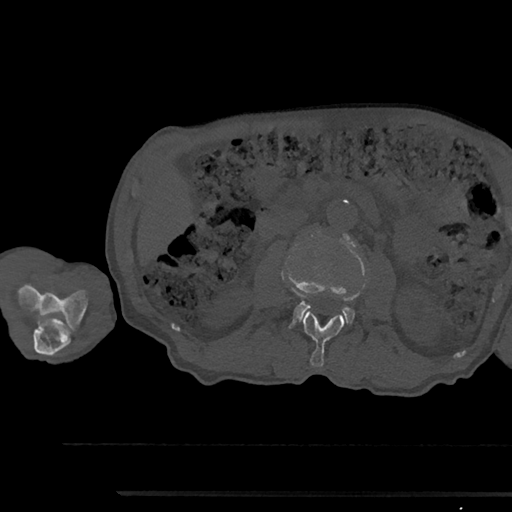
CT including the spine, one axial slice; slice 530 of 797 in the series (ordered by position); reconstruction kernel Br40s/3; bone window (W 1800 / L 400 HU); 0.5 mm slice thickness; 512 × 512 image matrix, field of view 367 × 367 mm. Male patient, age 79 years. Case-level facts recorded for this patient, not image findings: primary cancer: prostate.
Annotated regions visible in this slice (semi-automatic segmentation, software-assisted and operator-edited):
- L2 vertebra: bounding box [x1, y1, x2, y2] px = [301, 311, 345, 367]
- L3 vertebra: [285, 231, 366, 329]